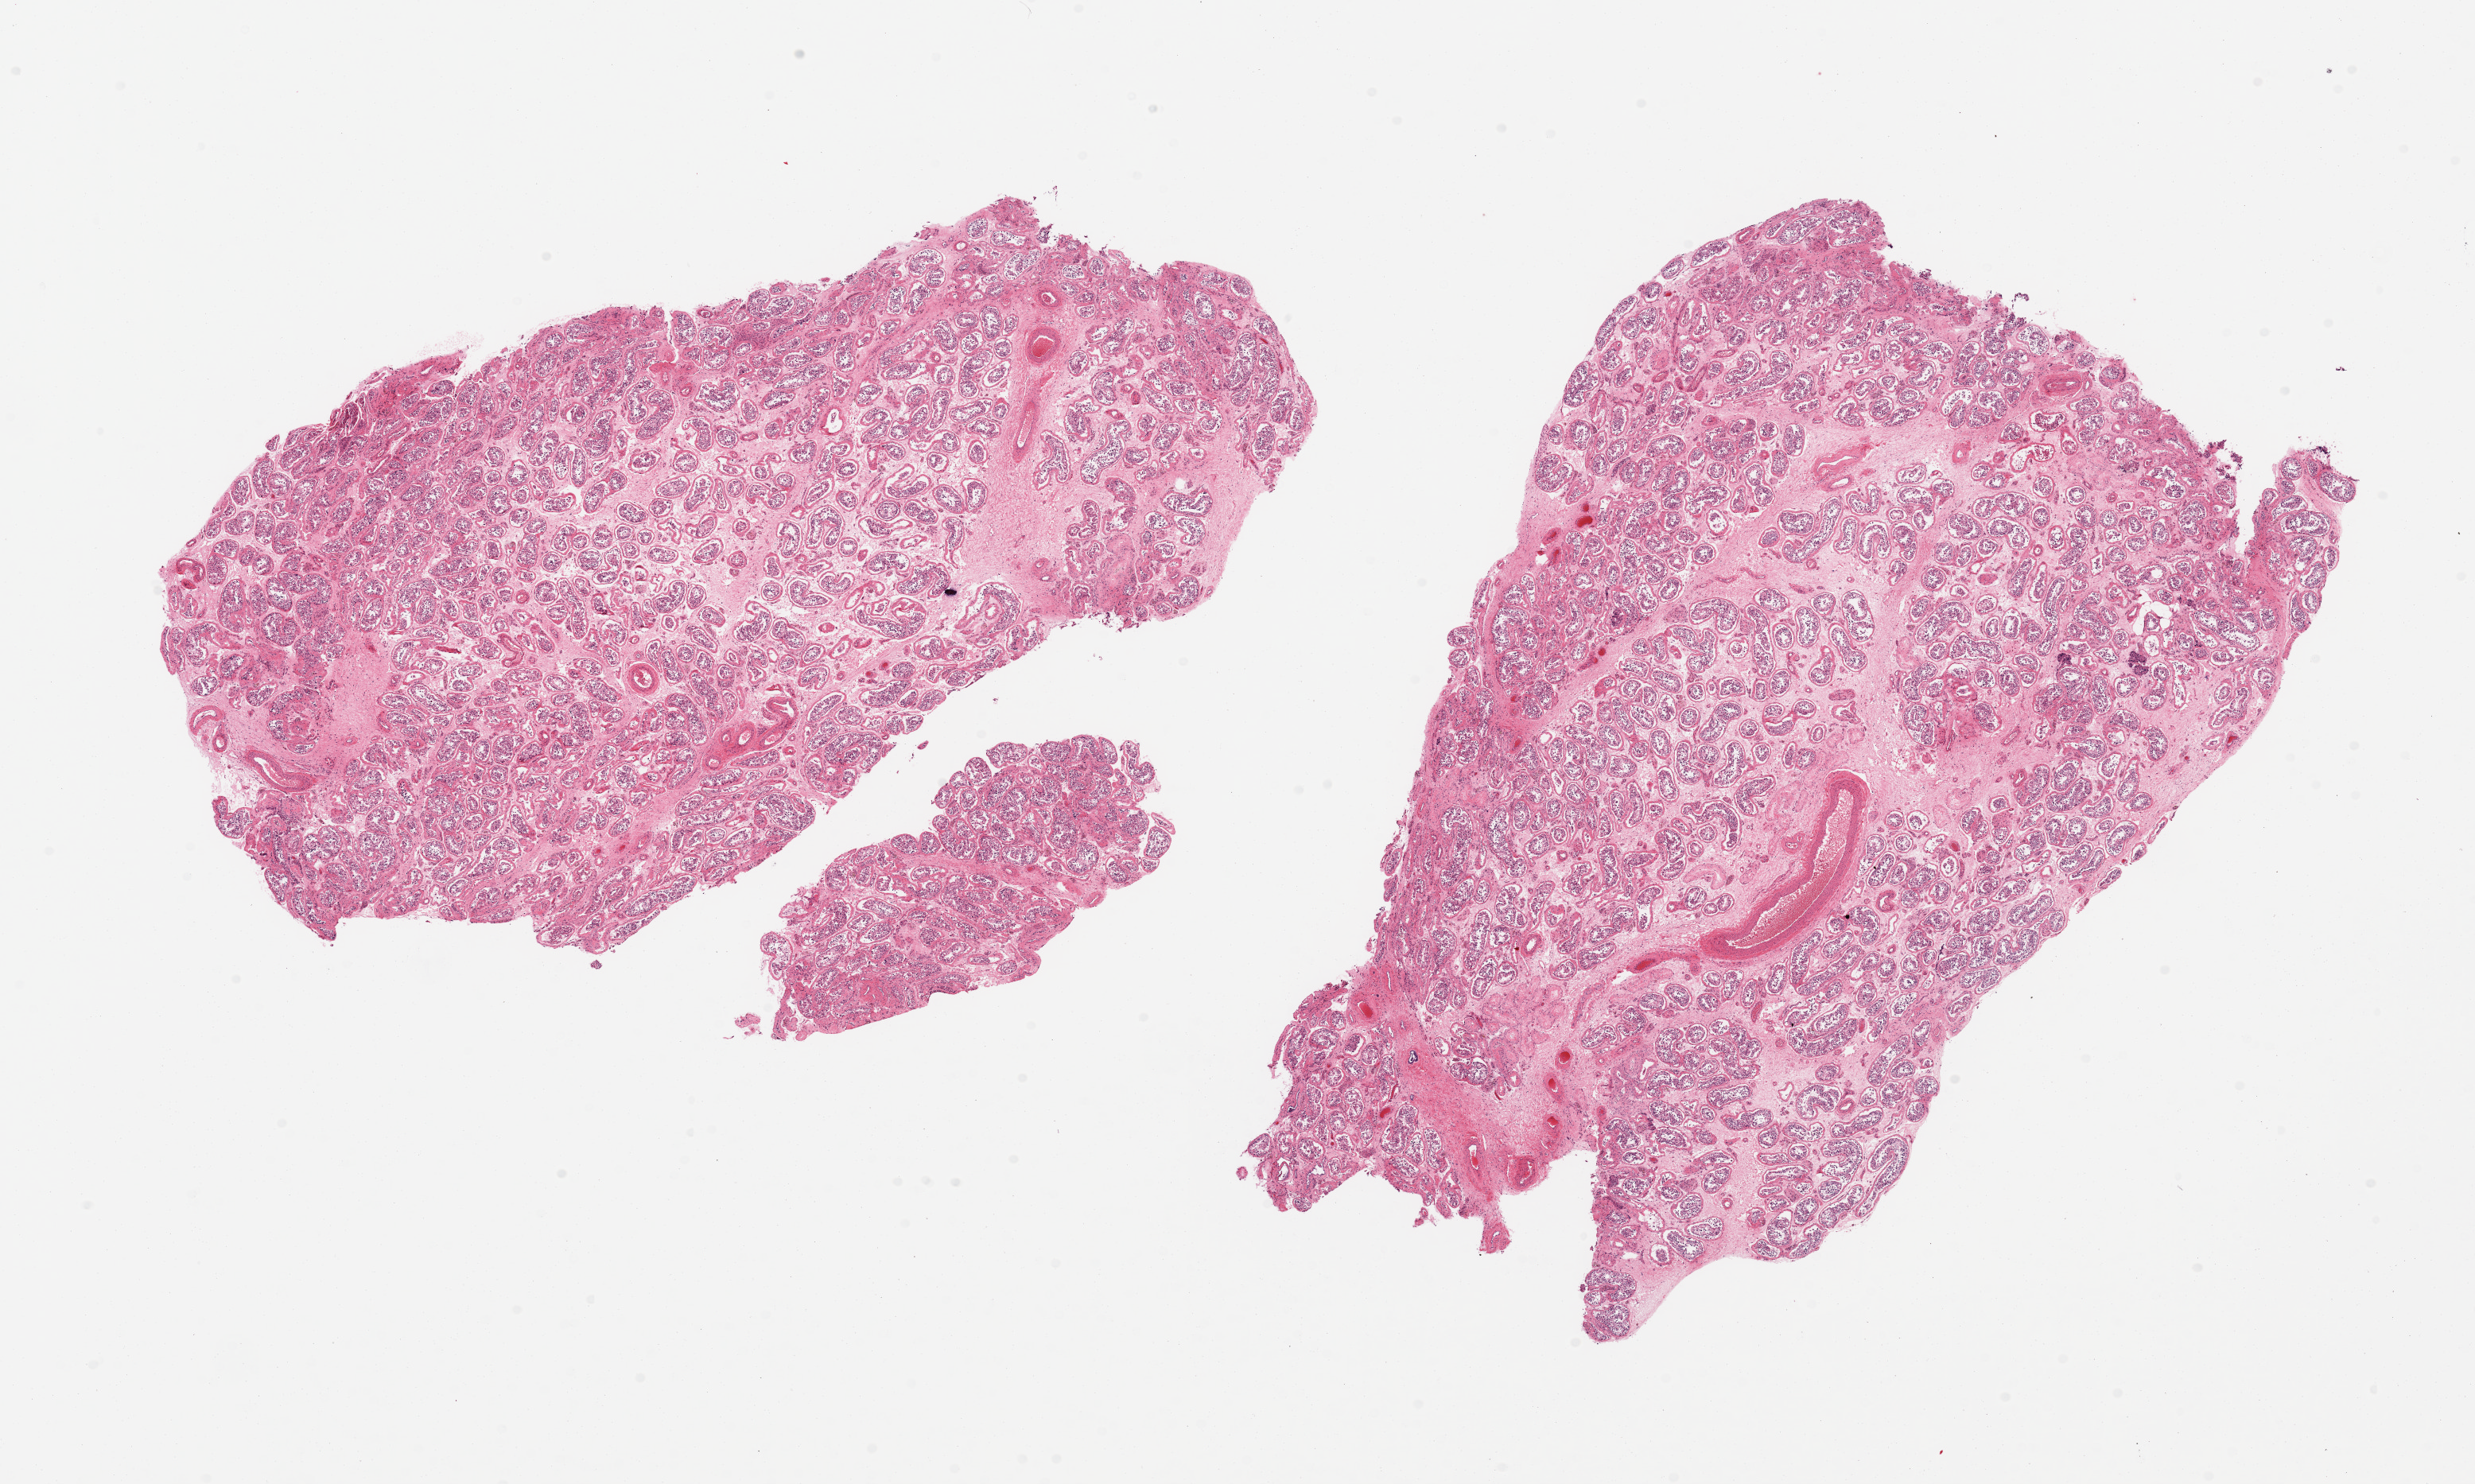
Whole-slide image, H&E stain, brightfield, whole scanned area (about 24.6 x 14.8 mm) shown as a low-resolution overview; PAXgene-fixed, paraffin-embedded tissue; target tissue: testis; donor tissue sample. Donor sex: male.
Pathologist's review note for this sample: 2 pieces; severe reduction in spermatogenesis; occasional hyalinized tubules.